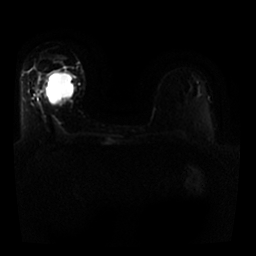
Breast MRI, one axial slice; diffusion-weighted series; image 2 of 4 stored at this slice position (different b-values; order by instance number); 1.5 T; 4 mm slice thickness; 256 × 256 image matrix, field of view 330 × 330 mm. Female patient.
Outlined on this slice (expert manual segmentation):
- tumour on diffusion-weighted imaging: bounding box <44,71,74,105> (left, top, right, bottom; pixels)